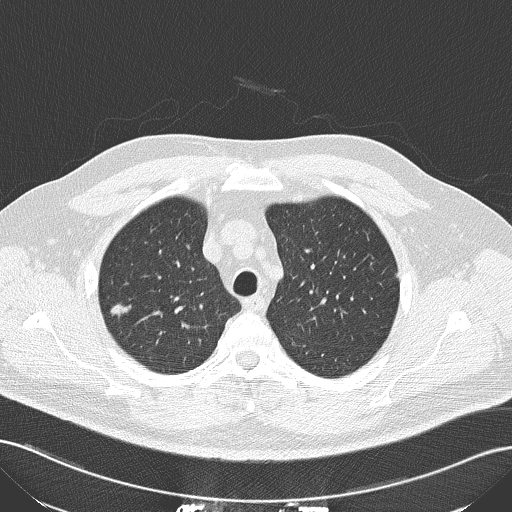
Low-dose screening chest CT, one axial slice. 120 kVp. Lung window (W 1500 / L -600 HU). 2 mm slice thickness. 512 × 512 image matrix, field of view 360 × 360 mm.
Structures marked on this image (manually delineated by an expert):
- lesion 1 (tumor, upper lobe of right lung): bounding box (x1, y1, x2, y2) in pixels: (110, 304, 131, 318)